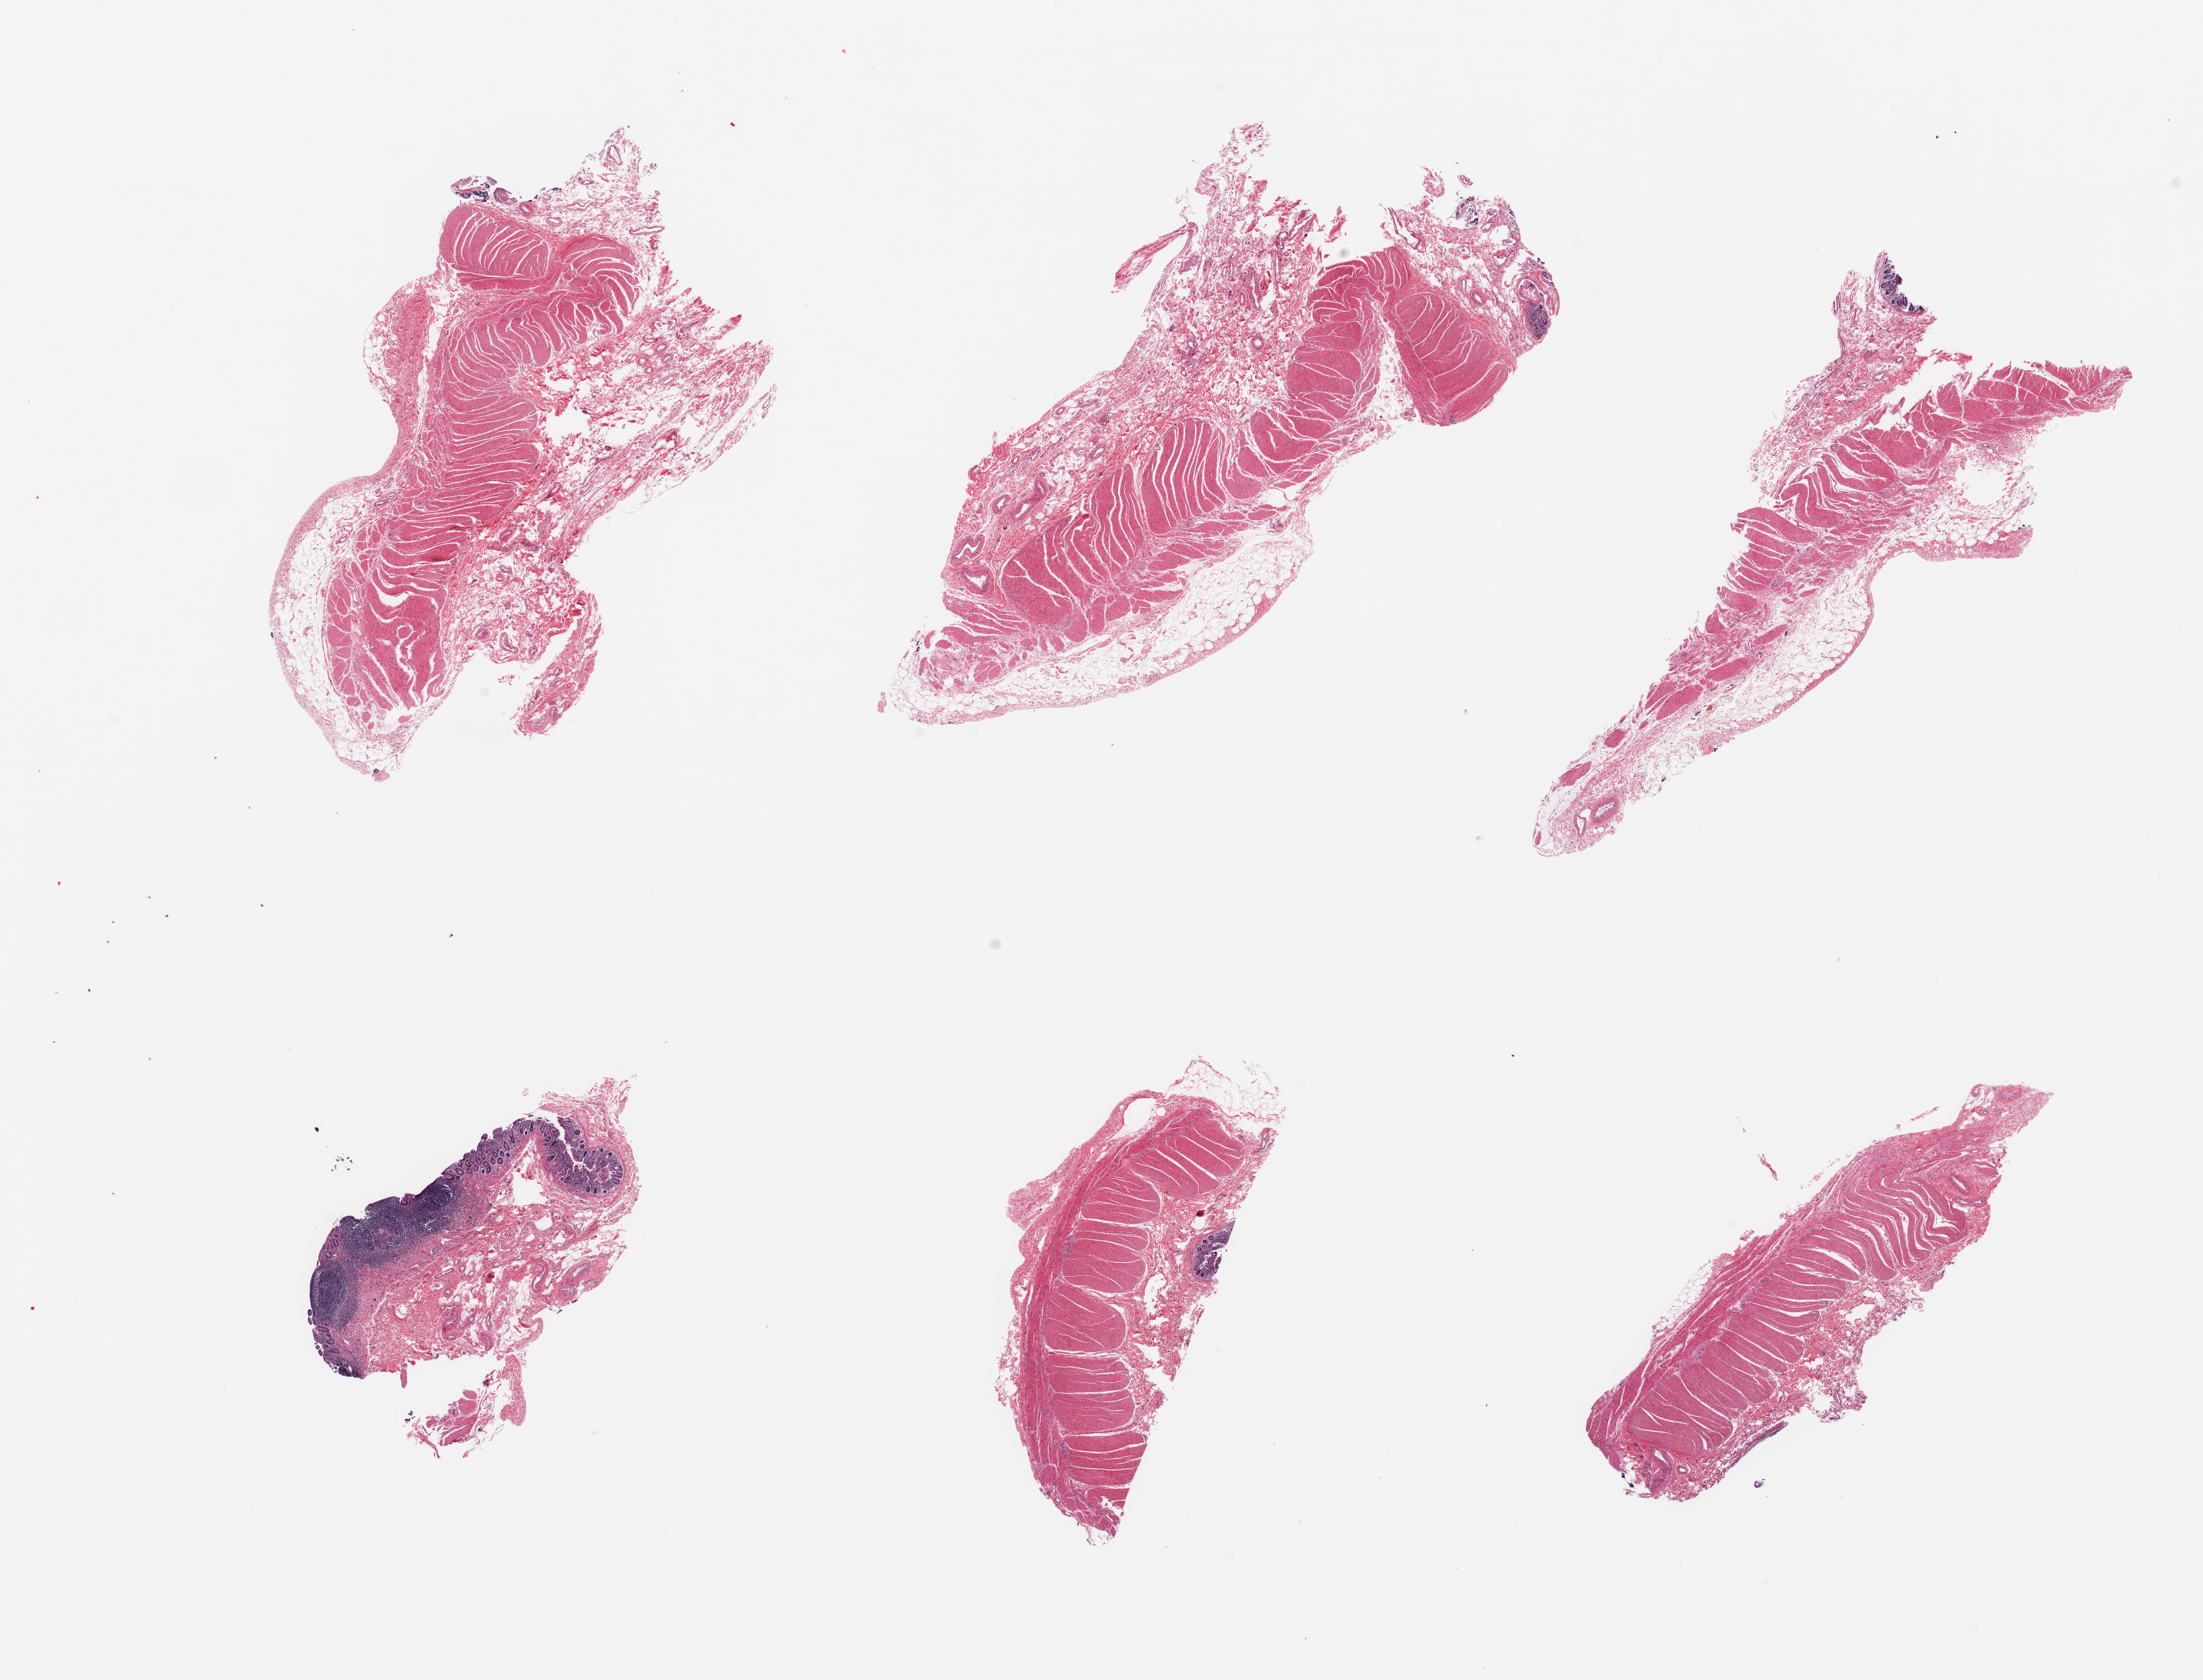
H&E whole-slide image, brightfield, shown as a low-resolution overview of the whole scanned area (about 22.6 x 17.3 mm, from a 20x scan). Donor: female.
Specimen: PAXgene-fixed paraffin-embedded (PFPE) section; target tissue: ileum; donor tissue sample.